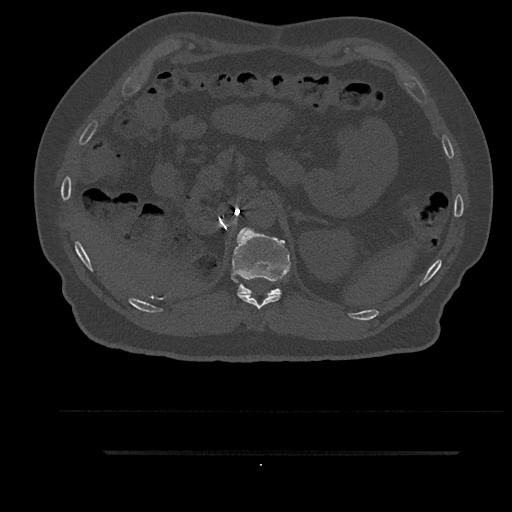
CT including the spine, one axial slice. Position 270 of 797 along the scan axis. 120 kVp. Bone window (W 1800 / L 400 HU). 0.5 mm slice thickness. 512 × 512 image matrix, field of view 432 × 432 mm. Patient: male, 63 years. From the clinical record (not read from this slice): primary cancer: renal.
Outlined on this slice (semi-automatic segmentation, software-assisted and operator-edited):
- T11 vertebra: bounding box (x1, y1, x2, y2) in pixels: (238, 294, 281, 309)
- T12 vertebra: (232, 228, 290, 296)